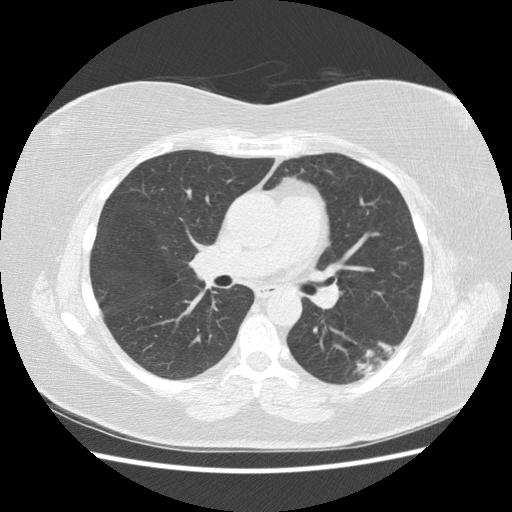
Low-dose screening chest CT, one axial slice. Position 87 of 151 along the scan axis. Reconstruction kernel STANDARD. 120 kVp. Lung window (W 1500 / L -600 HU). 2.5 mm slice thickness. 512 × 512 image matrix.
Annotated regions visible in this slice (manually delineated by an expert):
- lesion 1 (tumor, lower lobe of left lung): bounding box <357,341,400,376> (left, top, right, bottom; pixels)